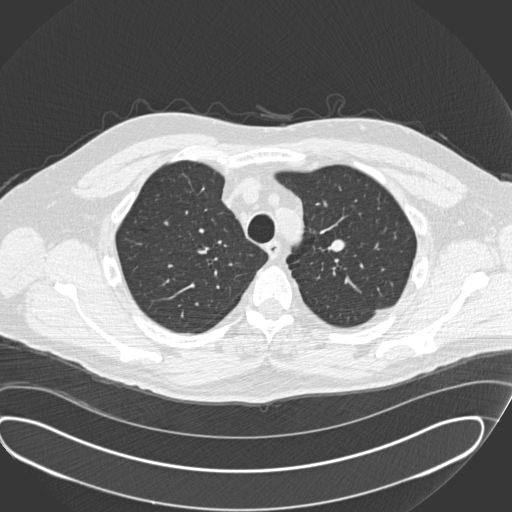
Axial slice from a low-dose chest CT screening exam. Second annual screen. Lung window (W 1500 / L -600 HU). 120 kVp. 512 × 512 image matrix. Male, age 56 years at enrolment. Current smoker at enrolment.
Expert reader's lesion annotation, bounding box (x1, y1, x2, y2) in pixels: (312, 225, 368, 270). No non-calcified nodule or mass ≥4 mm was recorded by the screening reader at this exam. Official screen result: negative screen, significant abnormalities not suspicious for lung cancer. Later outcome: lung cancer diagnosed 520 days after this screen (after the third annual screen) — neuroendocrine carcinoma, NOS, left upper lobe, well differentiated (G1), stage IA (AJCC 6th edition), 20 mm at pathology.